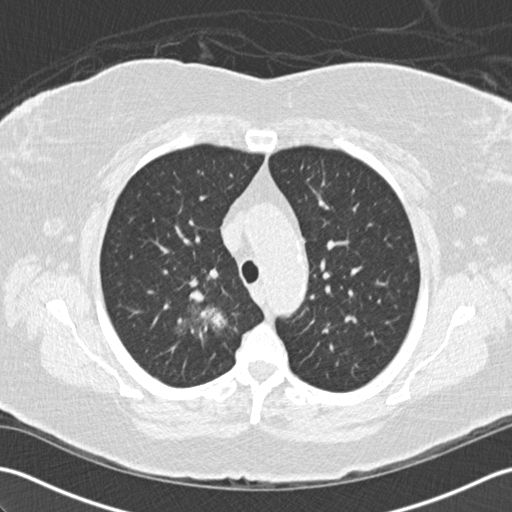
Axial slice from a low-dose chest CT screening exam; baseline screening round; lung window (W 1500 / L -600 HU); 2 mm slice thickness; 512 × 512 image matrix. Female participant, aged 72 years at enrolment. Former smoker at enrolment.
Lesion marked by an expert reader, bounding box <138,273,240,369> (left, top, right, bottom; pixels). The screening reader recorded 2 non-calcified nodules or masses ≥4 mm on this exam (right lower lobe, right lower lobe); which of them this box marks is not recorded. Participant outcome: lung cancer diagnosed 494 days after this screen (after the second annual screen) — bronchiolo-alveolar adenocarcinoma, NOS, right upper lobe, stage IIIB (AJCC 6th edition), 45 mm at pathology.